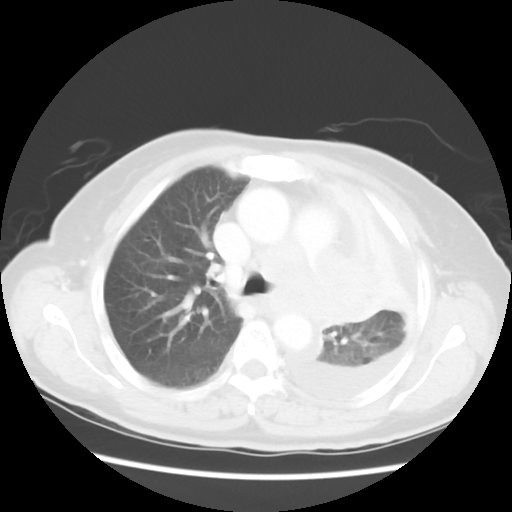
Chest CT, one axial slice; slice 36 of 52 in the series (ordered by position); reconstruction kernel STANDARD; 120 kVp; lung window (W 1500 / L -600 HU); 5 mm slice thickness; 512 × 512 image matrix. Patient: female, 72 years. From the clinical record (not read from this slice): clinical TNM (as recorded): T4 N3 M1b; histopathological grade: G3.
Structures marked on this image (rectangle marked by the reading radiologist):
- lung tumour (recorded histology: large cell carcinoma): bounding box <294,239,380,337> (left, top, right, bottom; pixels)